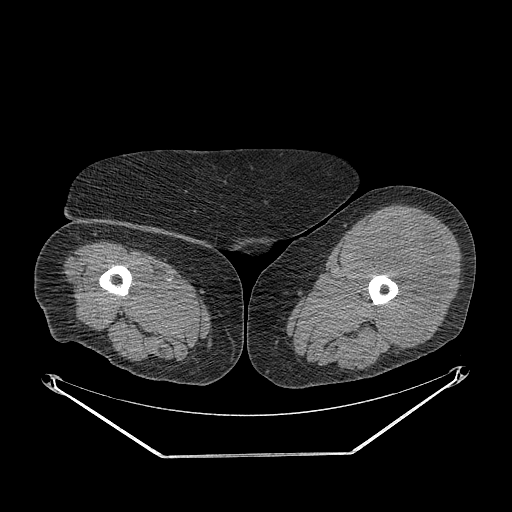
CT of an extremity soft-tissue mass (from a PET/CT study), one axial slice. Position 232 of 267 along the scan axis. 140 kVp. Soft-tissue window (W 400 / L 40 HU). 512 × 512 image matrix. Female patient. Case-level facts recorded for this patient, not image findings: histological type: undifferentiated – high grade; grade: high; site of the primary tumour: left thigh.
Outlined on this slice (expert contour drawn on MRI and transferred to this co-registered scan by the dataset authors):
- gross tumour volume including surrounding oedema: bounding box (x1, y1, x2, y2) in pixels: (354, 215, 451, 346)
- gross tumour volume (mass): (354, 215, 449, 346)